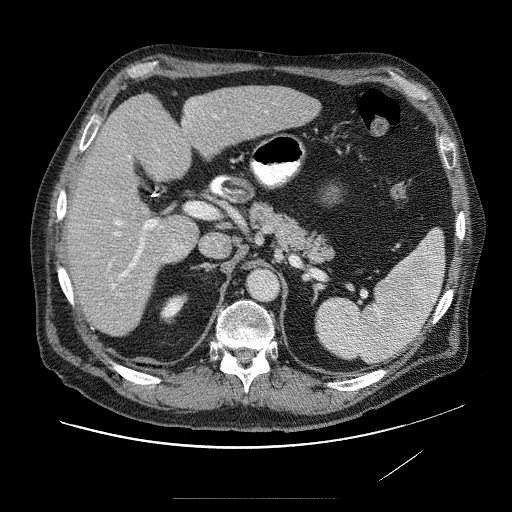
Contrast-enhanced abdominal CT (liver protocol), one axial slice; position 43 of 89 along the scan axis; reconstruction kernel STANDARD; soft-tissue window (W 400 / L 40 HU); 2.5 mm slice thickness; 512 × 512 image matrix. From the clinical record (not read from this slice): diagnosis: hepatocellular carcinoma (patient treated with transarterial chemoembolisation; whether this scan precedes or follows treatment is not stated here); TNM stage (as recorded): Stage-IVA; Child-Pugh class: A; tumour differentiation: moderately differentiated.
Outlined on this slice (semi-automatically segmented with operator editing):
- liver parenchyma outside the tumour (the mass and vessels are separate outlines, so this box may not span the whole liver): bounding box (x1, y1, x2, y2) in pixels: (64, 84, 326, 334)
- mass: (162, 233, 195, 264)
- liver vessels: (96, 113, 239, 329)